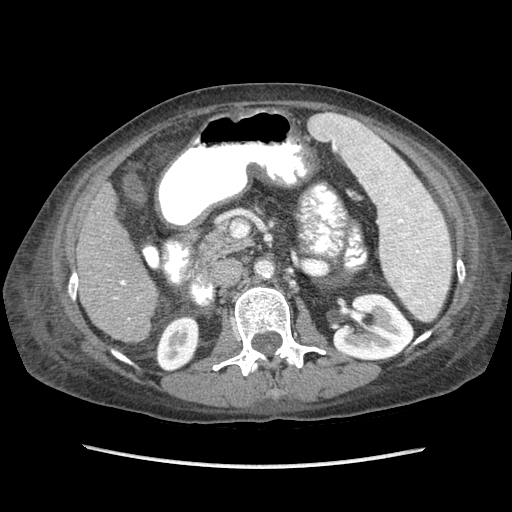
Contrast-enhanced abdominal CT (liver protocol), one axial slice; position 30 of 87 along the scan axis; reconstruction kernel STANDARD; soft-tissue window (W 400 / L 40 HU); 2.5 mm slice thickness; 512 × 512 image matrix, field of view 340 × 340 mm. Case-level facts recorded for this patient, not image findings: diagnosis: hepatocellular carcinoma (patient treated with transarterial chemoembolisation; whether this scan precedes or follows treatment is not stated here); TNM stage (as recorded): Stage-IIIB; Child-Pugh class: A; tumour differentiation: no biopsy.
Outlined on this slice (semi-automatically segmented with operator editing):
- liver parenchyma outside the tumour (the mass and vessels are separate outlines, so this box may not span the whole liver): bounding box [x1, y1, x2, y2] px = [76, 184, 158, 342]
- liver vessels: [114, 280, 130, 320]